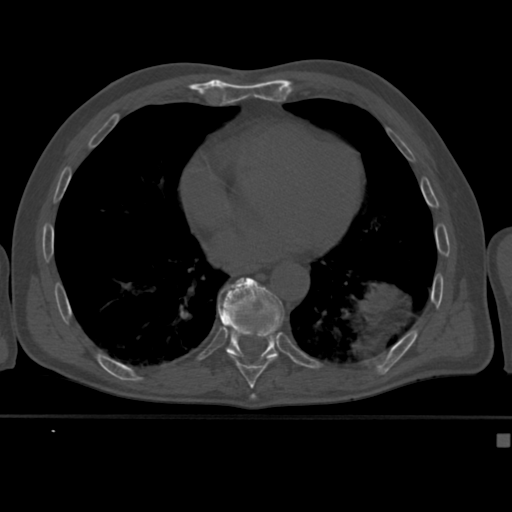
CT including the spine, one axial slice; slice 239 of 430 in the series (ordered by position); bone window (W 1800 / L 400 HU); 1.5 mm slice thickness; 512 × 512 image matrix, field of view 337 × 337 mm. Patient: male, 64 years. Case-level facts recorded for this patient, not image findings: primary cancer: uterus; vertebrae with lytic lesions (as recorded): T1, T4, T5, T7, L5.
Outlined on this slice (semi-automatically segmented with operator editing):
- T10 vertebra: bounding box (x1, y1, x2, y2) in pixels: (217, 277, 284, 365)
- T9 vertebra: (229, 354, 275, 382)